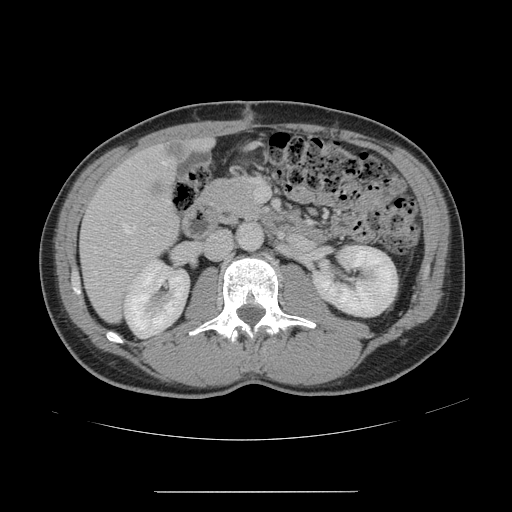
Contrast-enhanced abdominal CT, one axial slice; position 62 of 178 along the scan axis; soft-tissue window (W 400 / L 40 HU); 2.5 mm slice thickness; 512 × 512 image matrix, field of view 401 × 401 mm. Male patient, age 53 years. Case-level facts recorded for this patient, not image findings: diagnosis: colorectal cancer liver metastases, imaged before liver resection.
Outlined on this slice (manually delineated by an expert):
- hepatic veins: bounding box <95,161,166,274> (left, top, right, bottom; pixels)
- liver: <81,140,205,321>
- portal vein (with intrahepatic branches): <255,186,267,201>
- liver metastasis: <165,142,190,159>
- liver metastasis: <149,185,167,197>